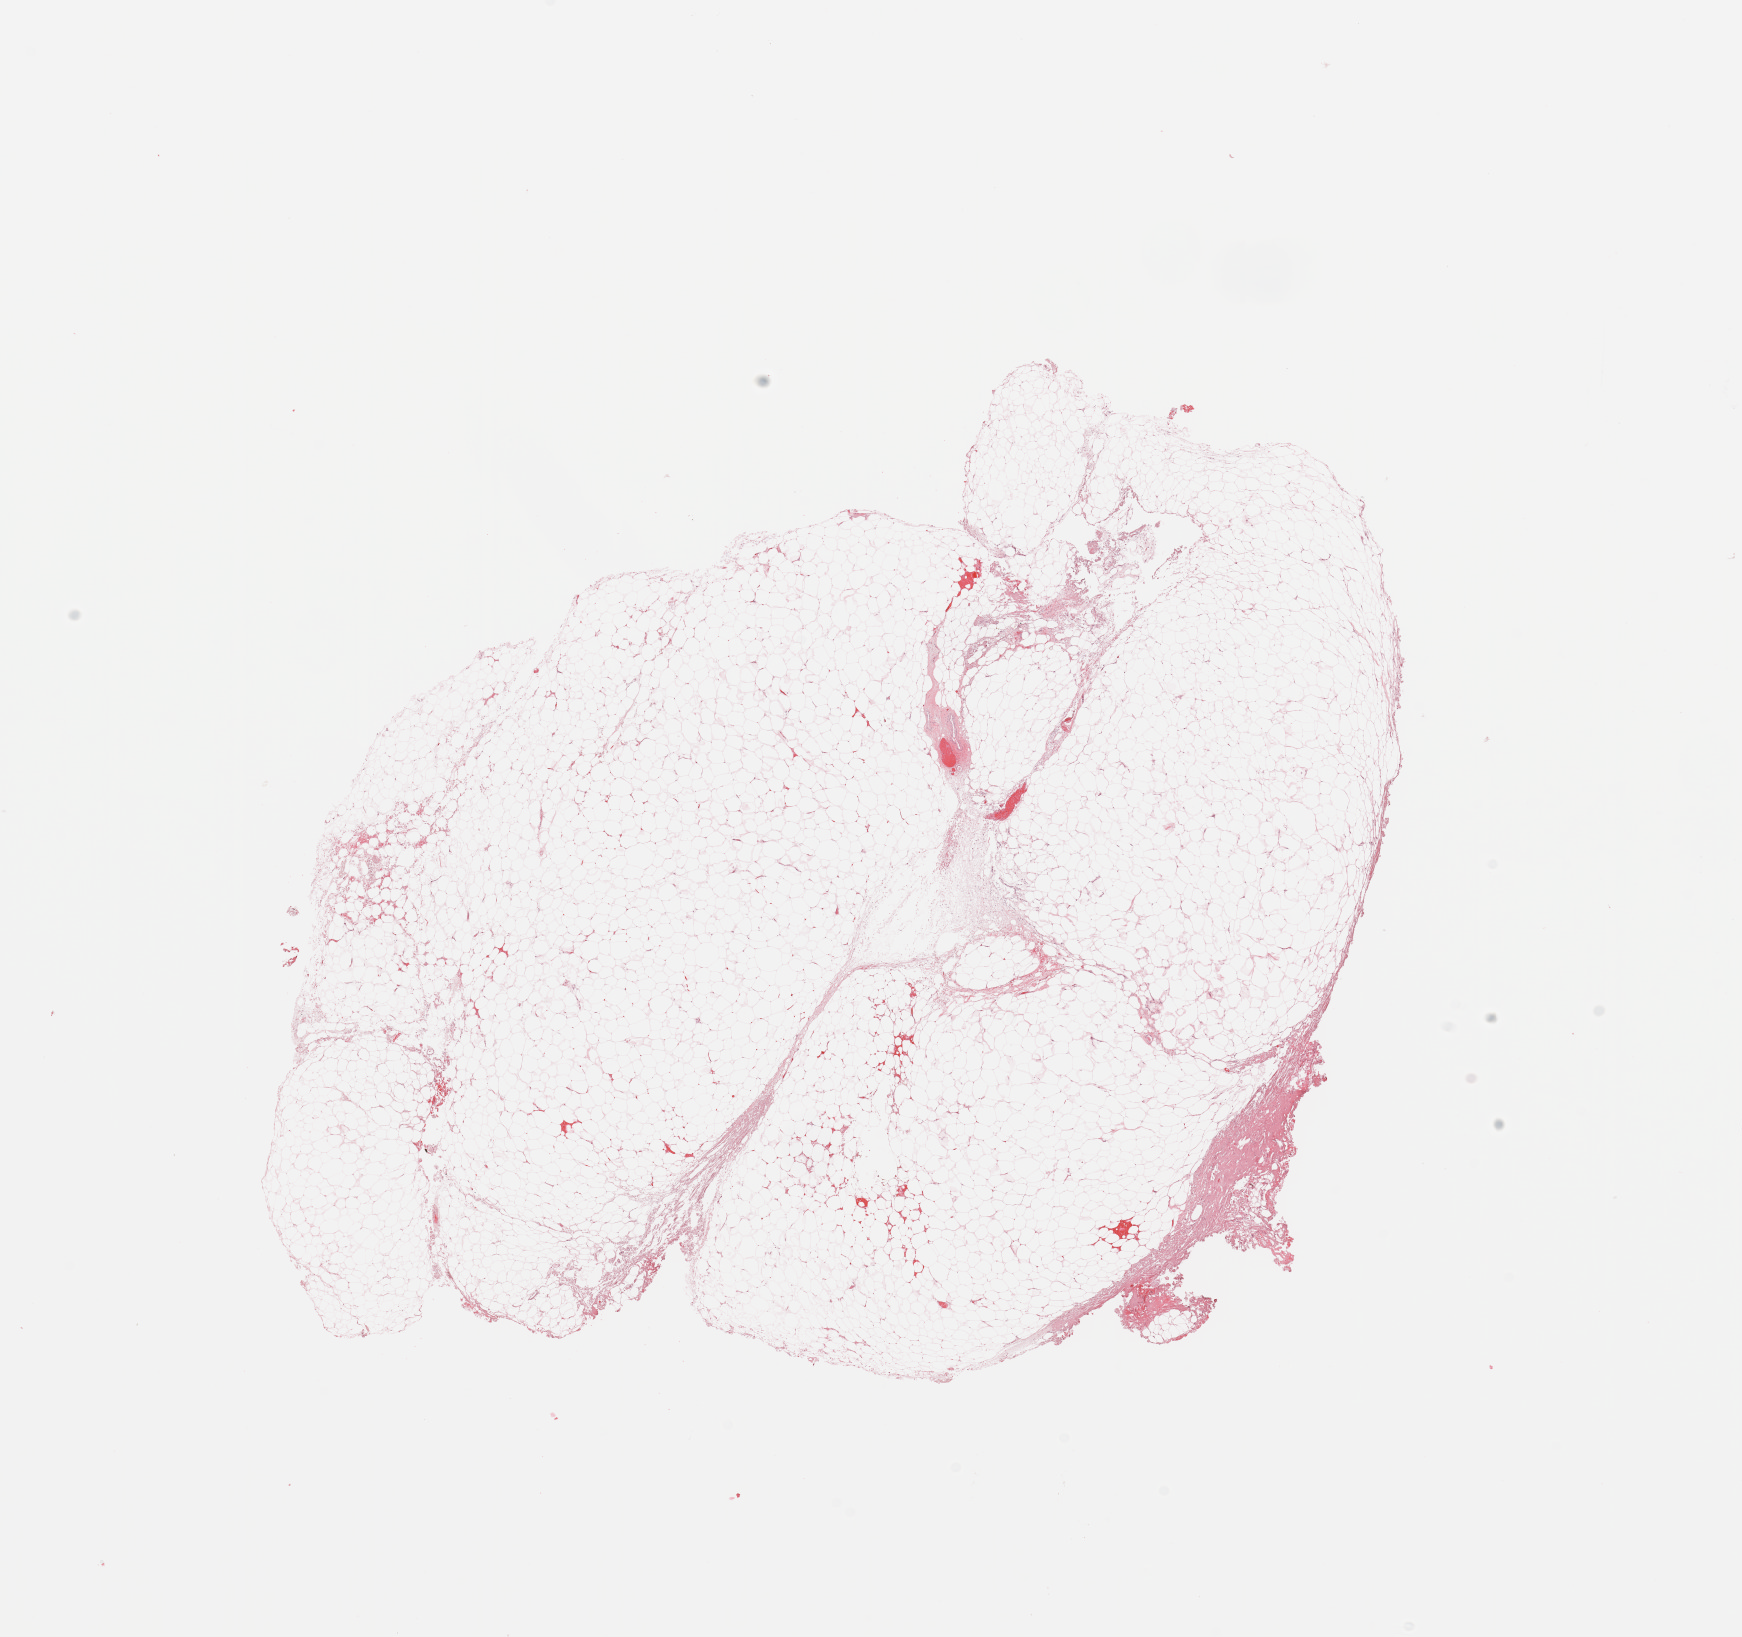
Digitized H&E-stained tissue section (whole slide), whole scanned area (about 13.8 x 13.0 mm, acquisition: 20x scan) shown as a low-resolution overview; normal (non-tumour) tissue sample, kidney. Patient: male, age 80 years.
- this section: normal (non-tumour) tissue from the same patient
- patient diagnosis: Renal cell carcinoma, NOS